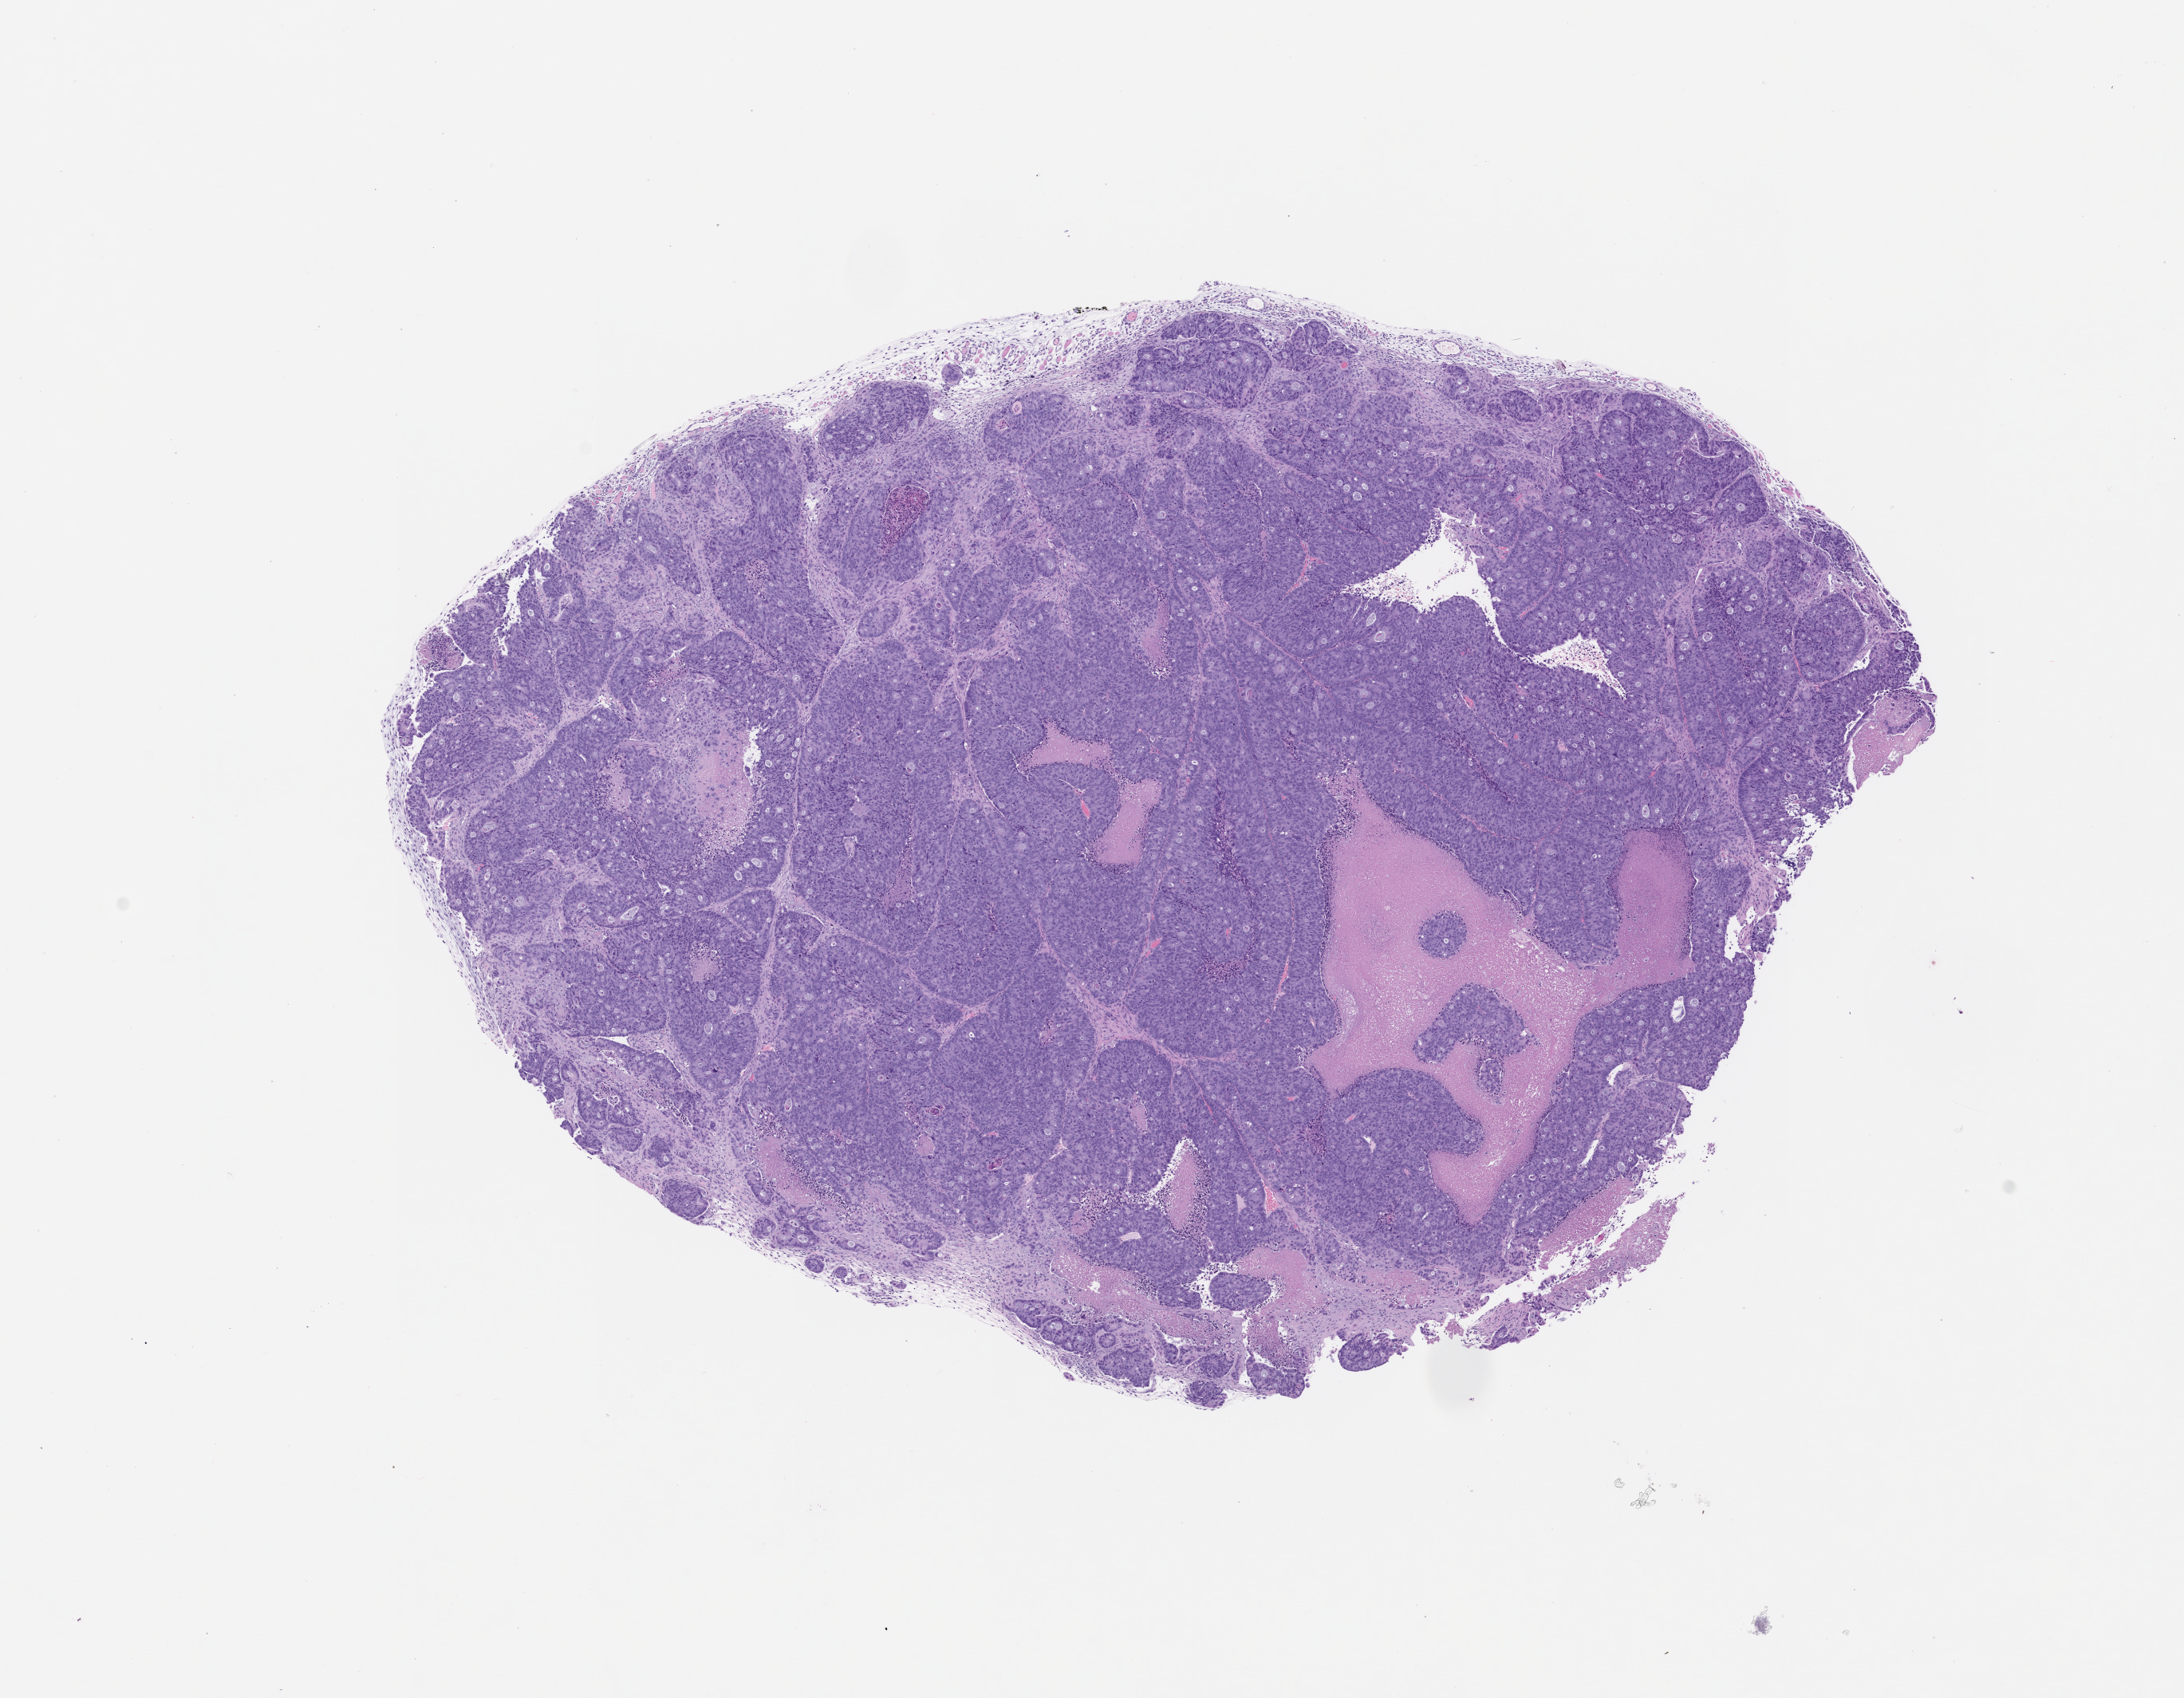
Hematoxylin and eosin (H&E) whole-slide image of a patient-derived xenograft (PDX) tumor grown in a mouse, passage 3, low-resolution overview of the scanned area, about 11.0 x 8.5 mm; formalin-fixed, paraffin-embedded (FFPE) tissue; tumor site category: colon.
Originating patient diagnosis: Colon Adenocarcinoma.